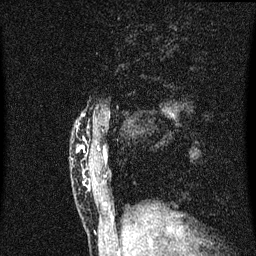
Breast MRI (dynamic contrast-enhanced), one sagittal slice. Slice 8 of 60 in the series (ordered by position). Dynamic contrast-enhanced series, image 2 of 3 at this slice position (ordered by acquisition). 1.5 T. TE 4.2 ms, TR 8.4 ms. 2 mm slice thickness. 256 × 256 image matrix, field of view 200 × 200 mm. Female patient, age 40 years.
Structures marked on this image (semi-automatically segmented with operator editing):
- analysis volume of interest (the breast-tissue region the enhancement analysis was run in; not a lesion): bounding box <78,114,102,203> (left, top, right, bottom; pixels)
- tumour enhancement mask (voxels above the 70 % enhancement threshold inside the analysis volume of interest): <78,146,86,153>